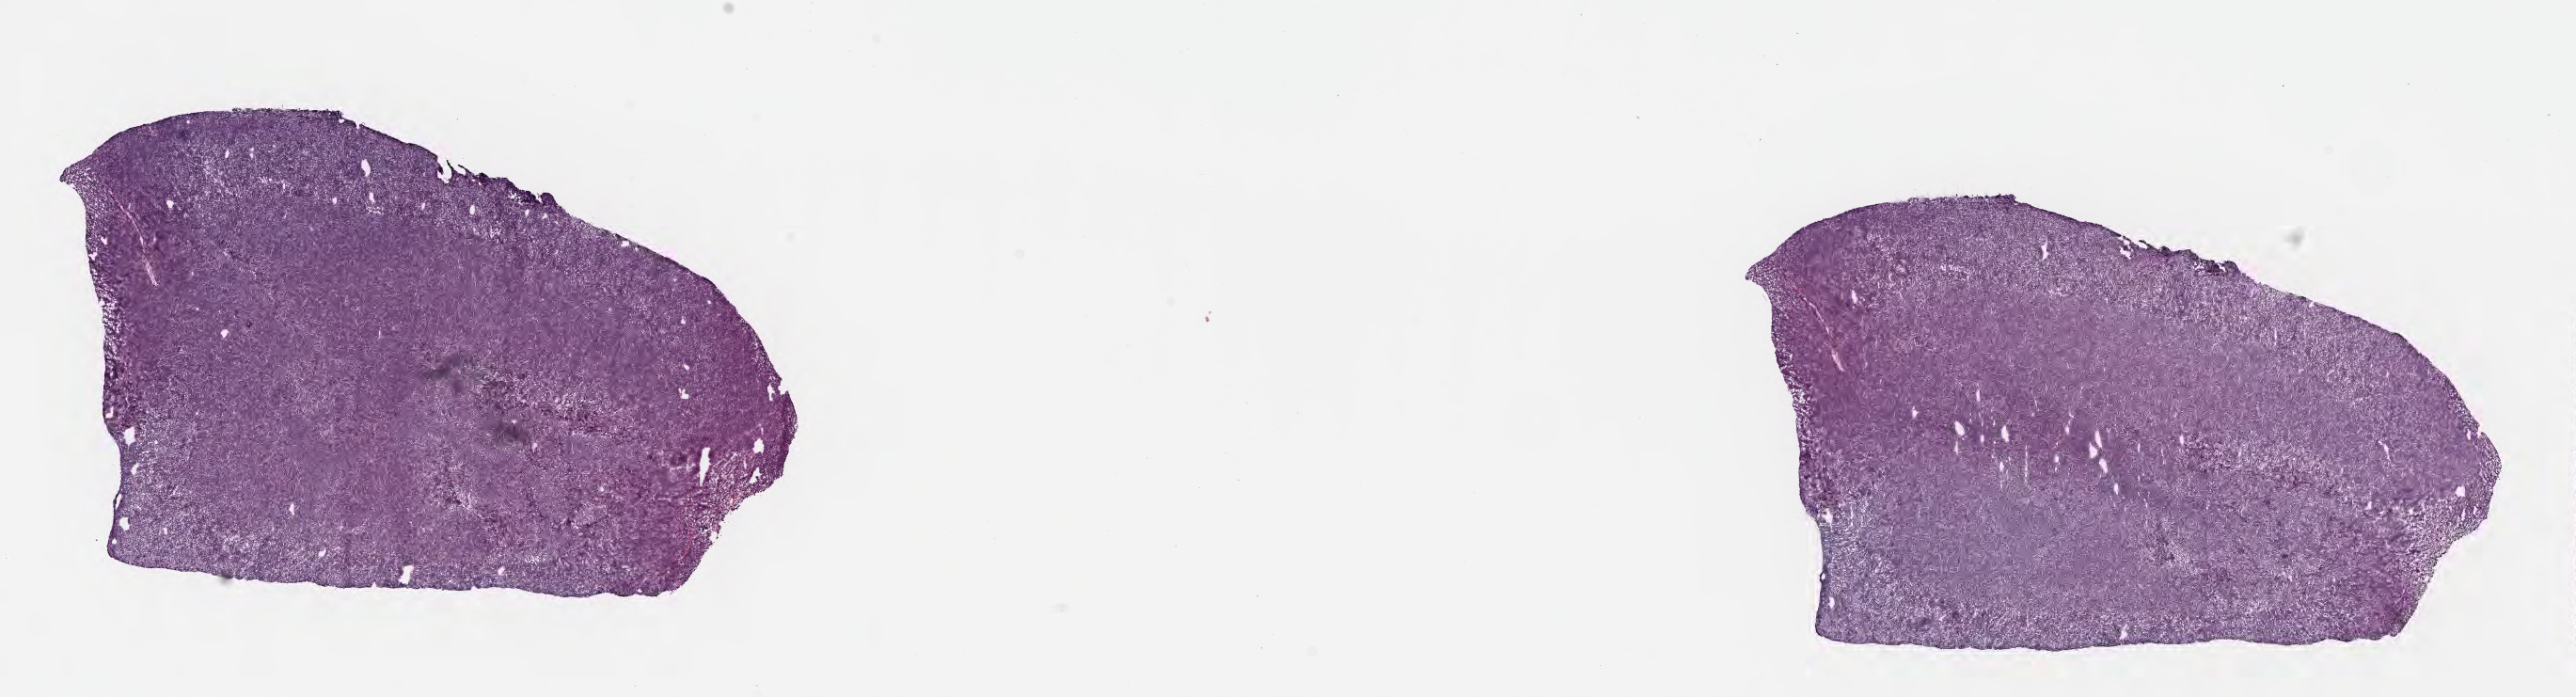
Digitized H&E-stained section — low-resolution overview of the scanned area, about 22.1 x 6.0 mm, frozen section (tissue freezing medium), primary tumor, anatomic site: cranium. Male patient; age at initial diagnosis 4 years. Pathologist review of this section (percent, as recorded): tumor cells 95%, tumor nuclei 95%, stromal cells 5%, necrosis 0%, normal cells 0%. Inflammatory infiltration, as recorded: lymphocyte infiltration 40%, monocyte infiltration 40%, neutrophil infiltration 5%.
Ann Arbor stage (patient): Stage IV. Section: top of the tissue portion. Diagnosis: Burkitt lymphoma, NOS.